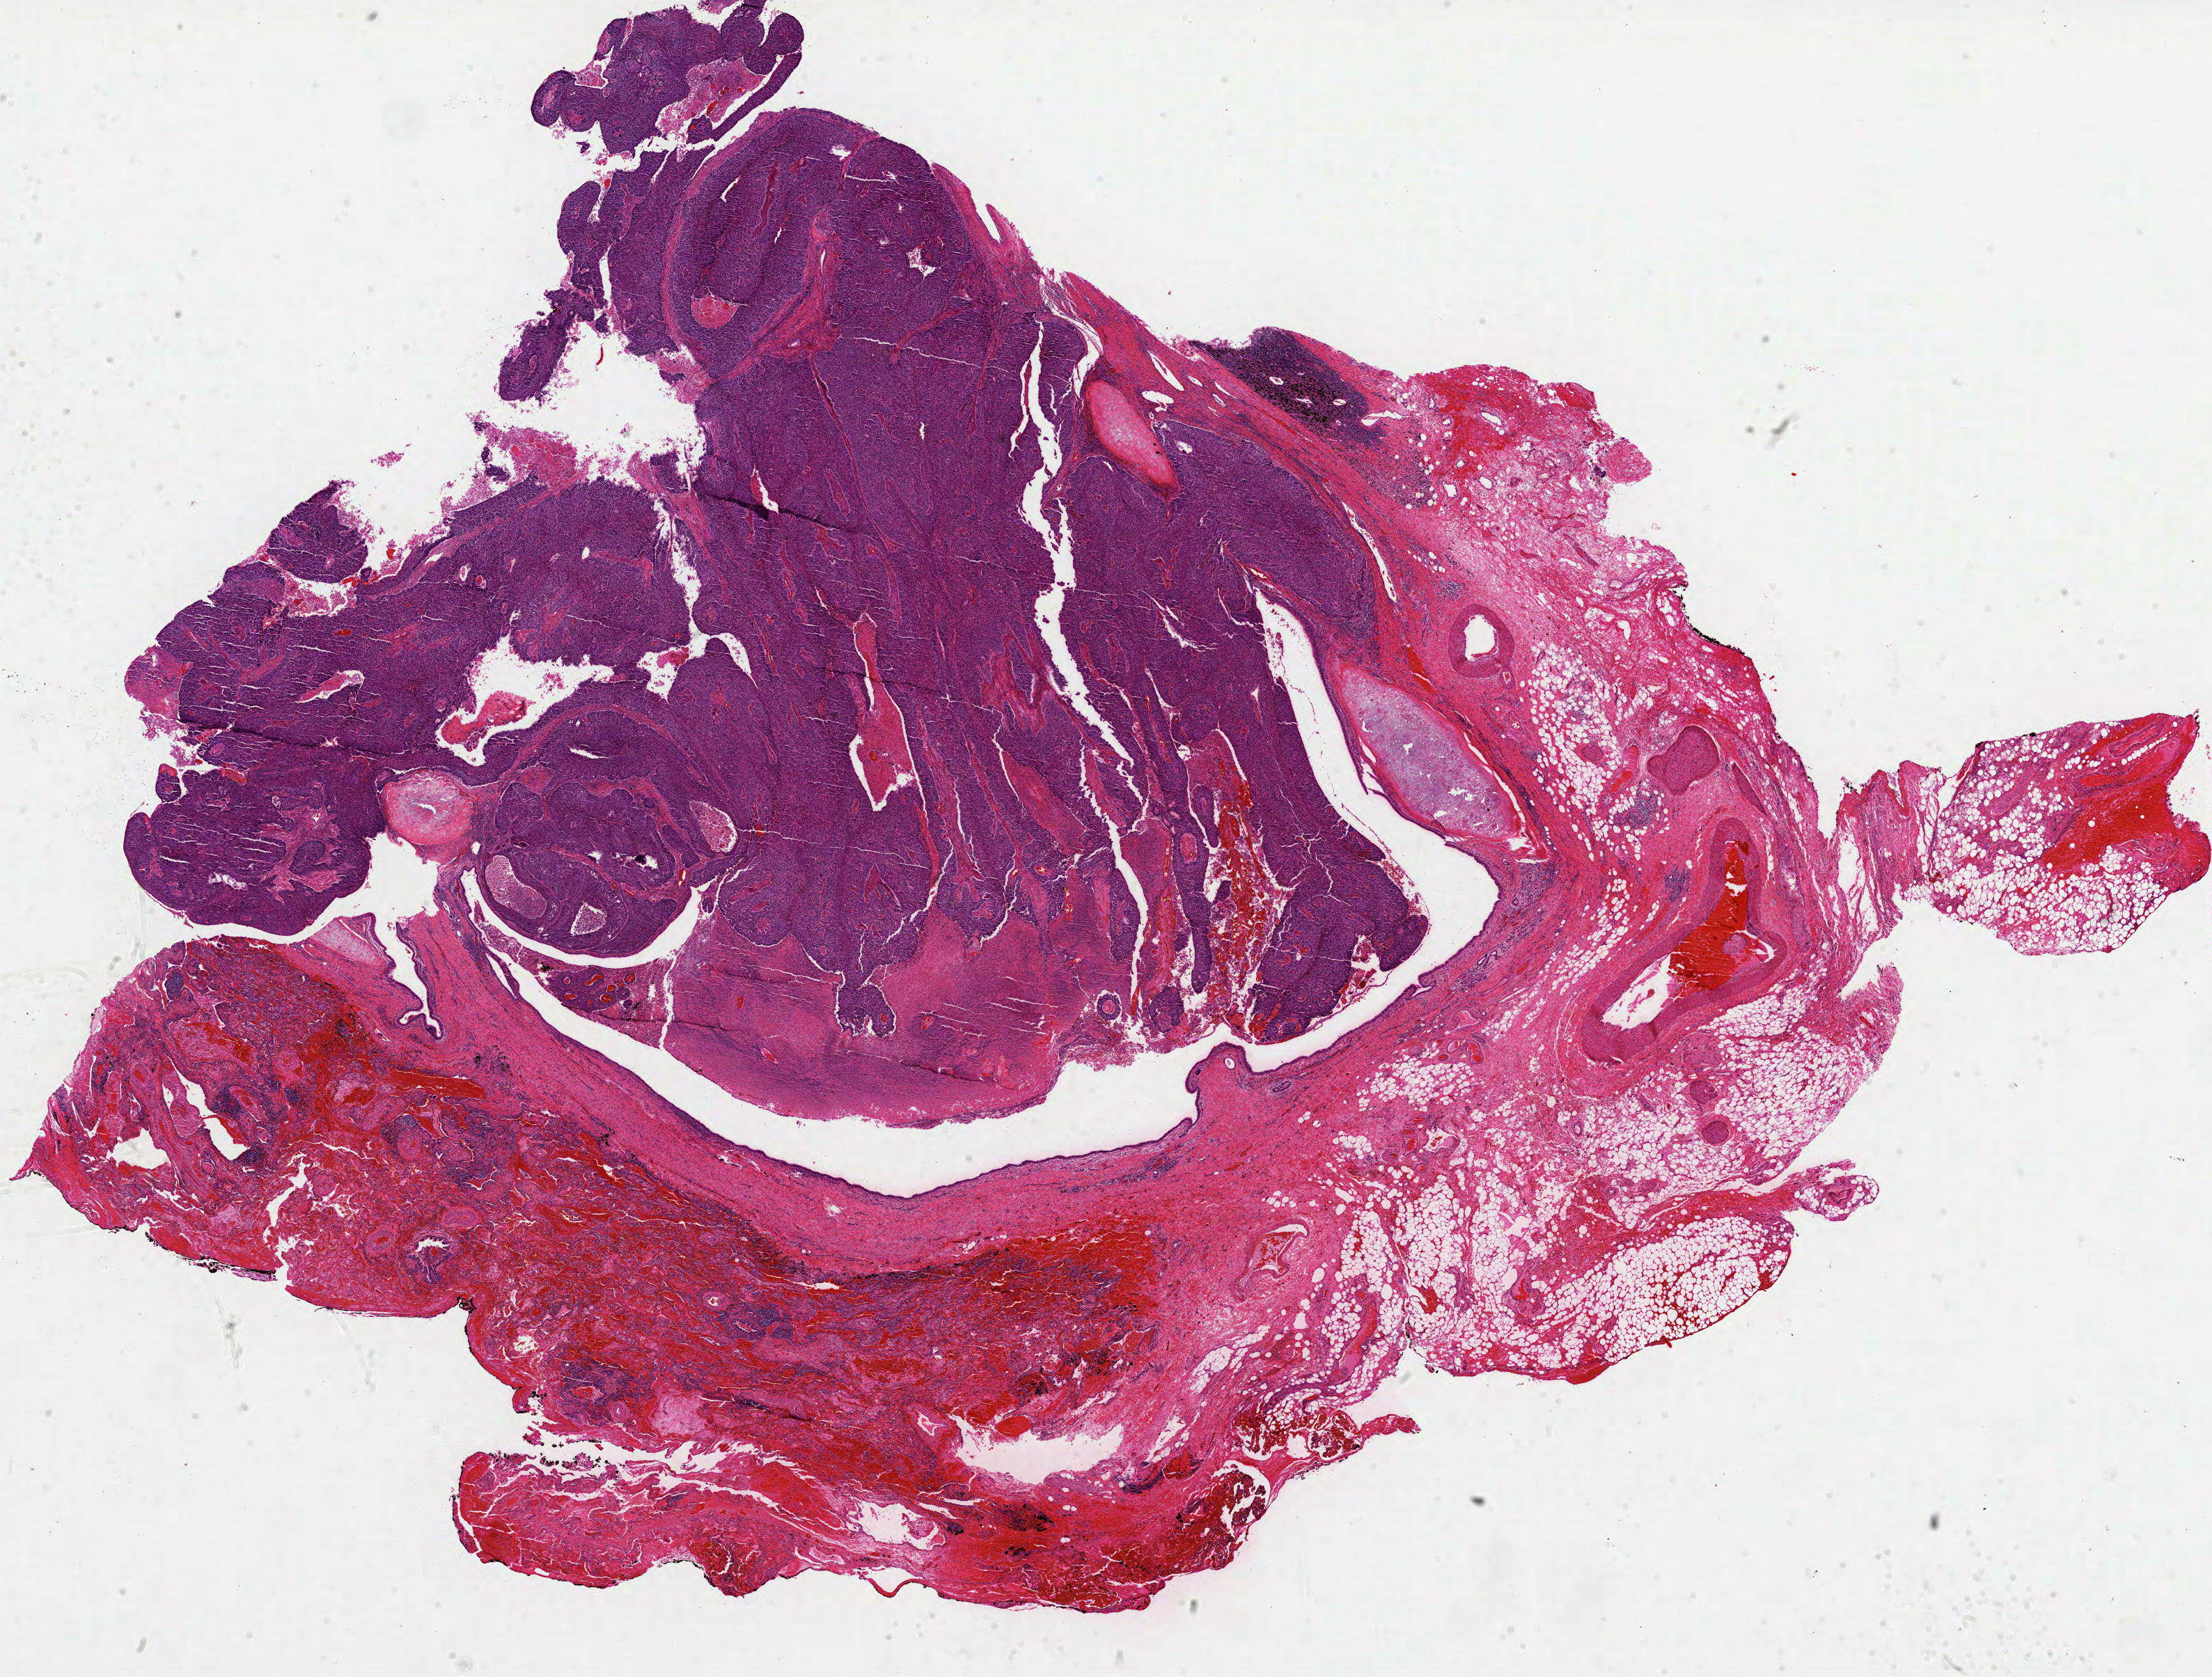
Whole-slide histology image, H&E-stained, low-resolution overview of the scanned area, about 25.6 x 19.4 mm, formalin-fixed paraffin-embedded (FFPE) diagnostic section, lung, primary tumour sample. Male, age 66 years at initial diagnosis.
Pathologic diagnosis: Squamous cell carcinoma, NOS (upper lobe, lung). AJCC pathologic stage: IIIA (6th edition). TNM: T2 N2 M0. Laterality: left.